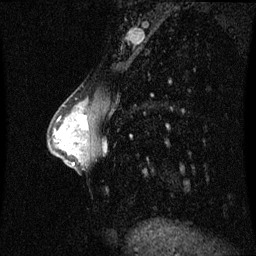
Breast MRI (dynamic contrast-enhanced), one sagittal slice. Dynamic contrast-enhanced series, image 2 of 3 at this slice position (ordered by acquisition). 1.5 T. TE 4.2 ms, TR 8.9 ms. 256 × 256 image matrix, field of view 210 × 210 mm. Female patient, age 33 years. From the clinical record (not read from this slice): setting: breast cancer imaged before/during neoadjuvant chemotherapy; receptor status: HER2-positive.
Structures marked on this image (semi-automatically segmented with operator editing):
- analysis volume of interest (the breast-tissue region the enhancement analysis was run in; not a lesion): box from (x=66, y=102) to (x=95, y=141) px
- tumour enhancement mask (voxels above the 70 % enhancement threshold inside the analysis volume of interest): (x=78, y=116)–(x=88, y=130)